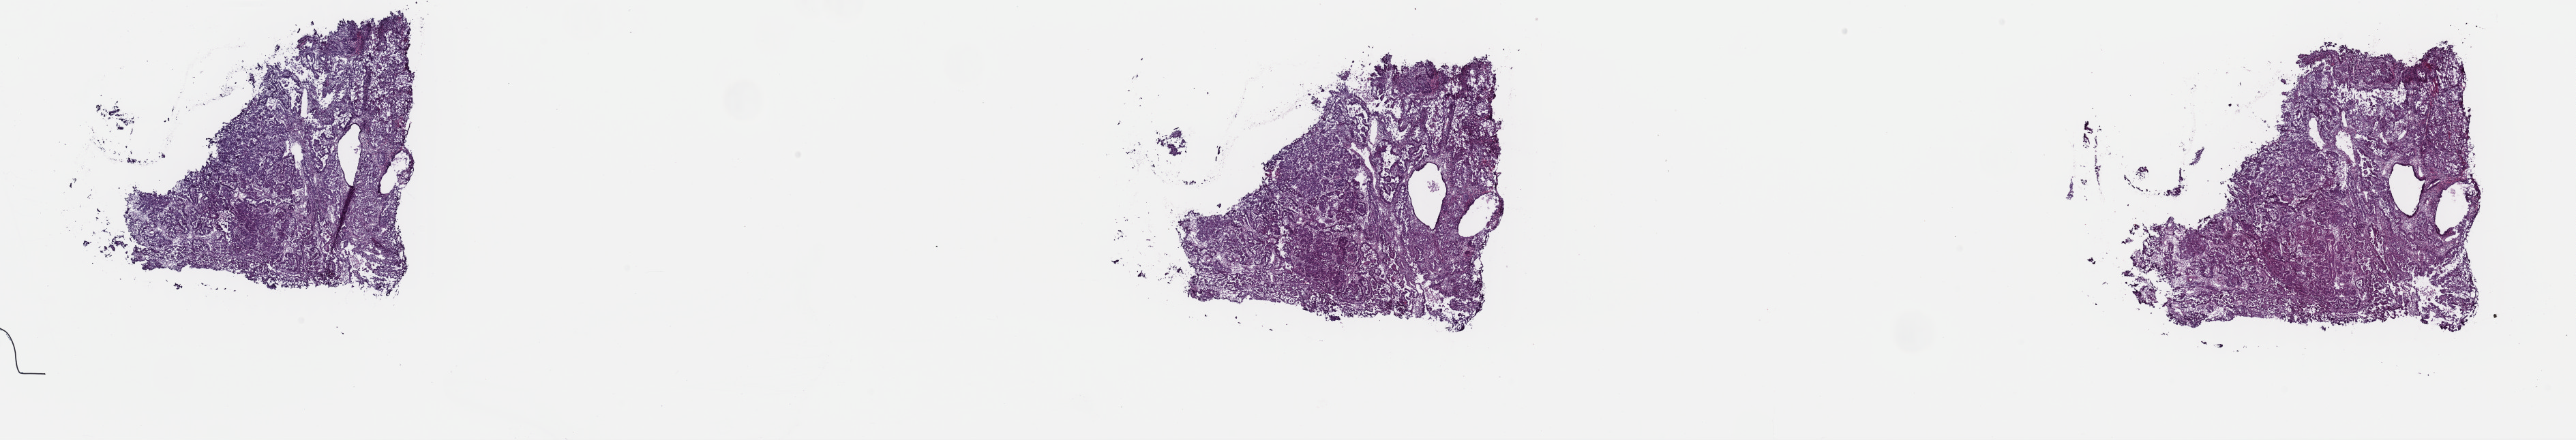
Digitized H&E-stained tissue section (whole slide) — a low-resolution overview of the entire scanned area, about 29.8 x 5.1 mm (acquisition: 40x scan), frozen section from the top of the tissue portion, primary tumour sample from the uterus. Patient: female, age at initial diagnosis 61 years. Slide review estimates, as recorded: tumour cells 70%, tumour nuclei 75%.
Pathologic diagnosis: Serous cystadenocarcinoma, NOS (endometrium).